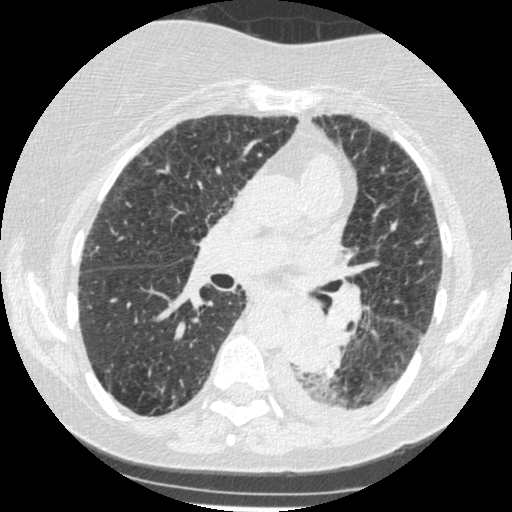
Low-dose screening chest CT, one axial slice. Position 139 of 341 along the scan axis. Reconstruction kernel STANDARD. Lung window (W 1500 / L -600 HU). 1.25 mm slice thickness. 512 × 512 image matrix, field of view 310 × 310 mm.
Structures marked on this image (expert manual segmentation):
- lesion 1 (tumor, lower lobe of left lung): bounding box <285,308,339,374> (left, top, right, bottom; pixels)